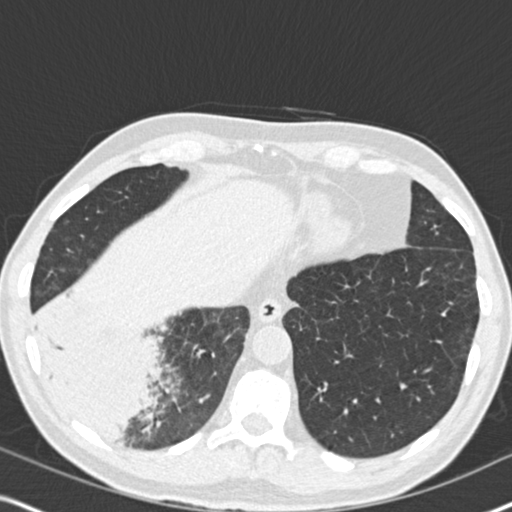
Low-dose screening chest CT, axial slice; second annual screen; lung window (W 1500 / L -600 HU); 2 mm slice thickness; slice 127 of 182 in the series. Male participant, aged 61 years at enrolment. Current smoker at enrolment.
Lesion marked by an expert reader, bounding box [x1, y1, x2, y2] px = [25, 288, 182, 456]. The exam's reader record, not a measurement of the box and not confirmed to be the same lesion: non-calcified nodule or mass ≥4 mm, right lower lobe, 90 × 80 mm, soft tissue attenuation, pre-existing on the prior screen: yes; interval growth: yes. Official screen result: positive, other. Later outcome: lung cancer diagnosed 20 days after this screen — bronchiolo-alveolar adenocarcinoma, NOS, right lower lobe, moderately differentiated (G2), stage IIIB (AJCC 6th edition), 90 mm at pathology.